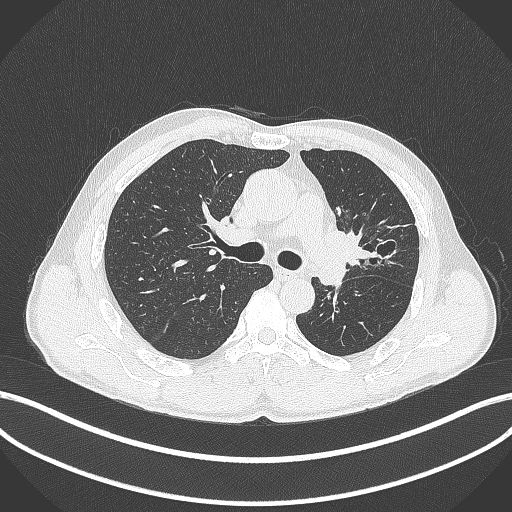
Chest CT, one axial slice. Slice 265 of 429 in the series (ordered by position). 120 kVp. Lung window (W 1500 / L -600 HU). 512 × 512 image matrix. Patient: male, 57 years. From the clinical record (not read from this slice): clinical TNM (as recorded): T2b N0 M0.
Annotated regions visible in this slice (bounding box drawn by a radiologist):
- lung tumour (recorded histology: squamous cell carcinoma): bounding box (x1, y1, x2, y2) in pixels: (322, 228, 379, 269)